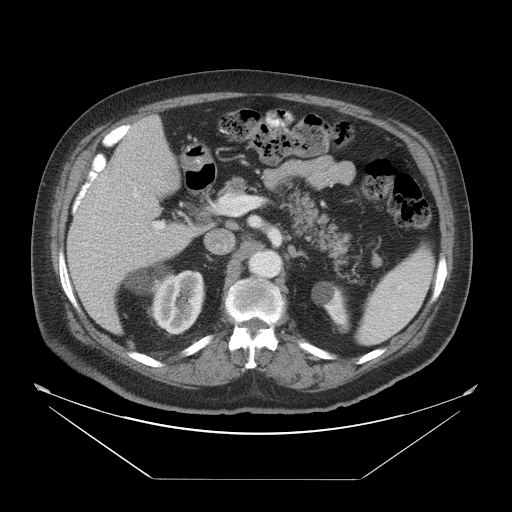
Contrast-enhanced abdominal CT, one axial slice; slice 27 of 45 in the series (ordered by position); 120 kVp; soft-tissue window (W 400 / L 40 HU); 5 mm slice thickness; 512 × 512 image matrix, field of view 463 × 463 mm. Male patient, age 87 years. From the clinical record (not read from this slice): diagnosis: colorectal cancer liver metastases, imaged before liver resection; multiple liver metastases: no; largest metastasis: 4.5 cm; chemotherapy before resection: no.
Annotated regions visible in this slice (manually delineated by an expert):
- liver: box from (x=67, y=115) to (x=196, y=335) px
- planned liver remnant (the part of the liver to remain after resection): (x=126, y=115)–(x=171, y=154)
- portal vein (with intrahepatic branches): (x=133, y=193)–(x=164, y=239)
- liver metastasis: (x=166, y=169)–(x=181, y=189)
- liver metastasis: (x=104, y=160)–(x=119, y=180)